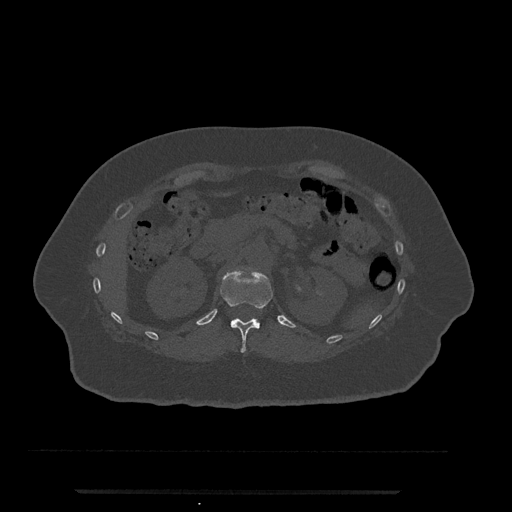
CT including the spine, one axial slice. Reconstruction kernel Br40s/3. Bone window (W 1800 / L 400 HU). 0.5 mm slice thickness. 512 × 512 image matrix, field of view 440 × 440 mm. Female patient, age 51 years. From the clinical record (not read from this slice): primary cancer: neuro; vertebrae with lytic lesions (as recorded): T8.
Annotated regions visible in this slice (semi-automatically segmented with operator editing):
- T12 vertebra: bounding box <220,267,273,353> (left, top, right, bottom; pixels)